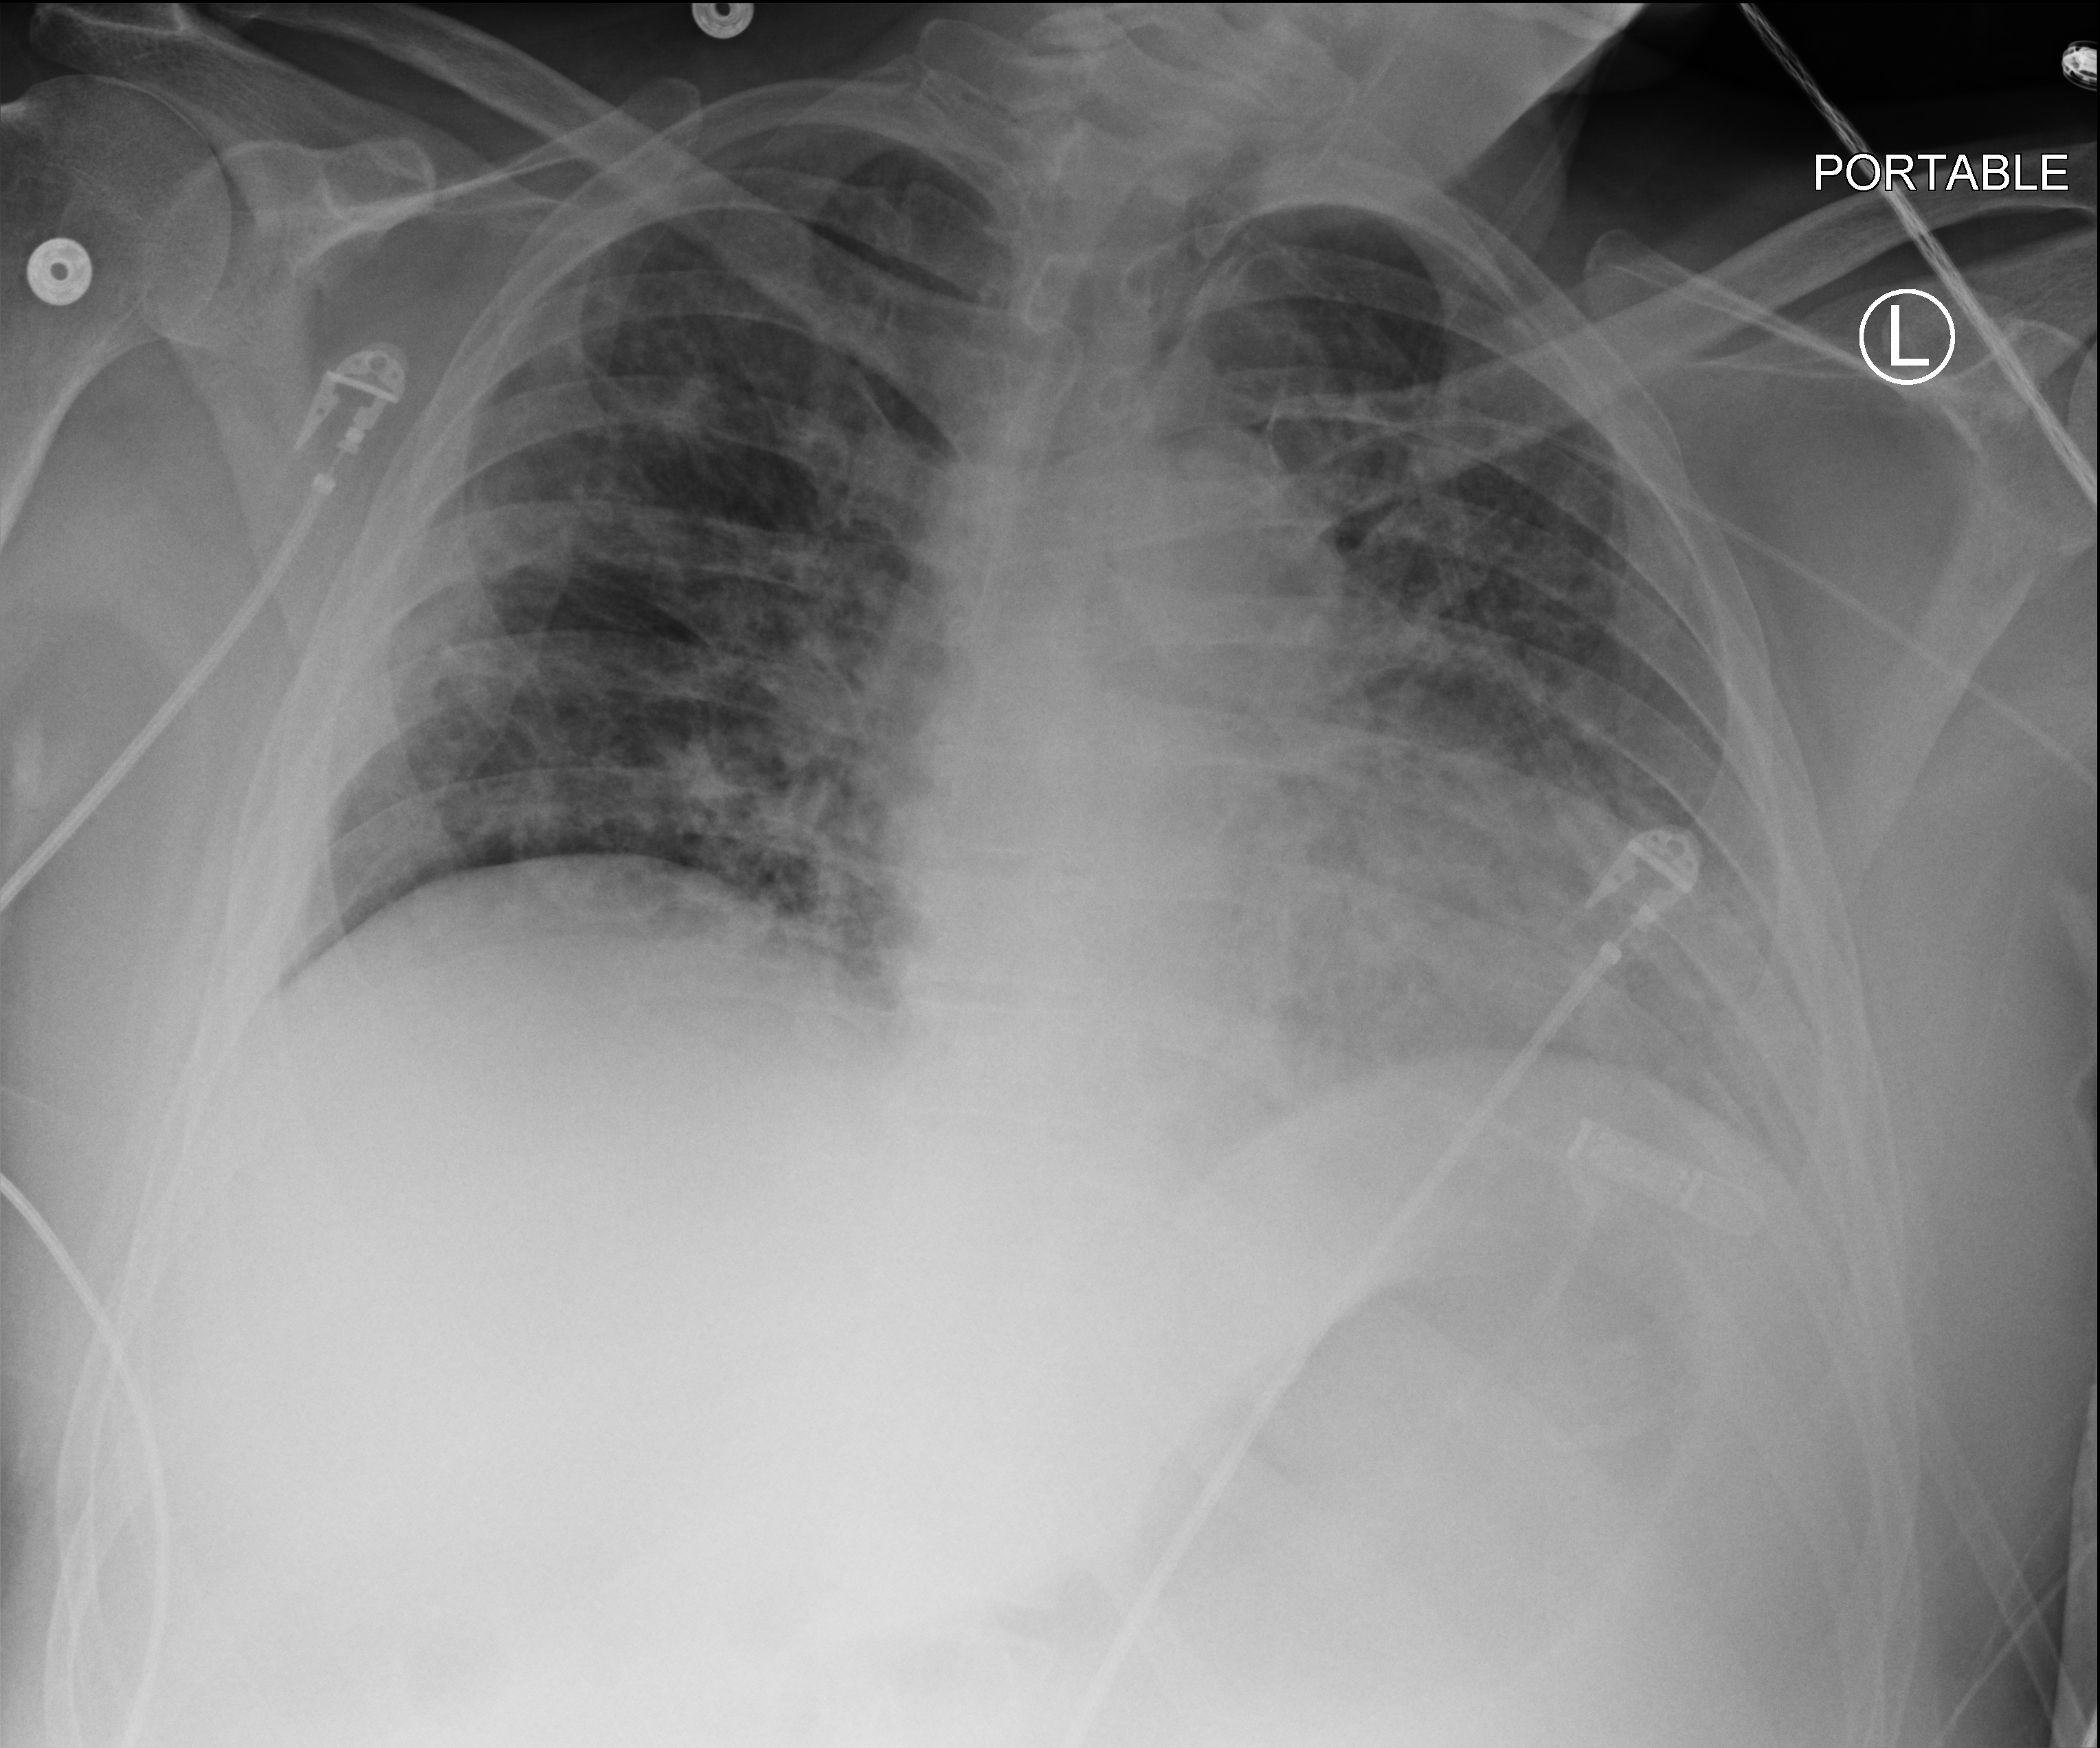
Chest X-ray (portable); anteroposterior (AP) projection. Male patient hospitalised with COVID-19, age 18–59 years.
Hospital-stay facts (about this admission, not read from this image; timing relative to this image not recorded):
- length of hospital stay: 39 days